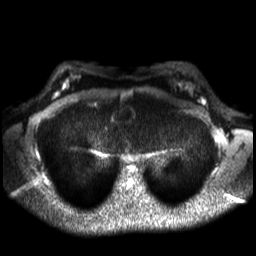
Breast MRI, one axial slice; position 23 of 30 along the scan axis; diffusion-weighted series; image 2 of 4 stored at this slice position (different b-values; order by instance number); 3 T; 4 mm slice thickness; 256 × 256 image matrix, field of view 320 × 320 mm. Female patient.
Annotated regions visible in this slice (outlined manually by an expert reader):
- tumour on diffusion-weighted imaging: bounding box <200,98,206,105> (left, top, right, bottom; pixels)